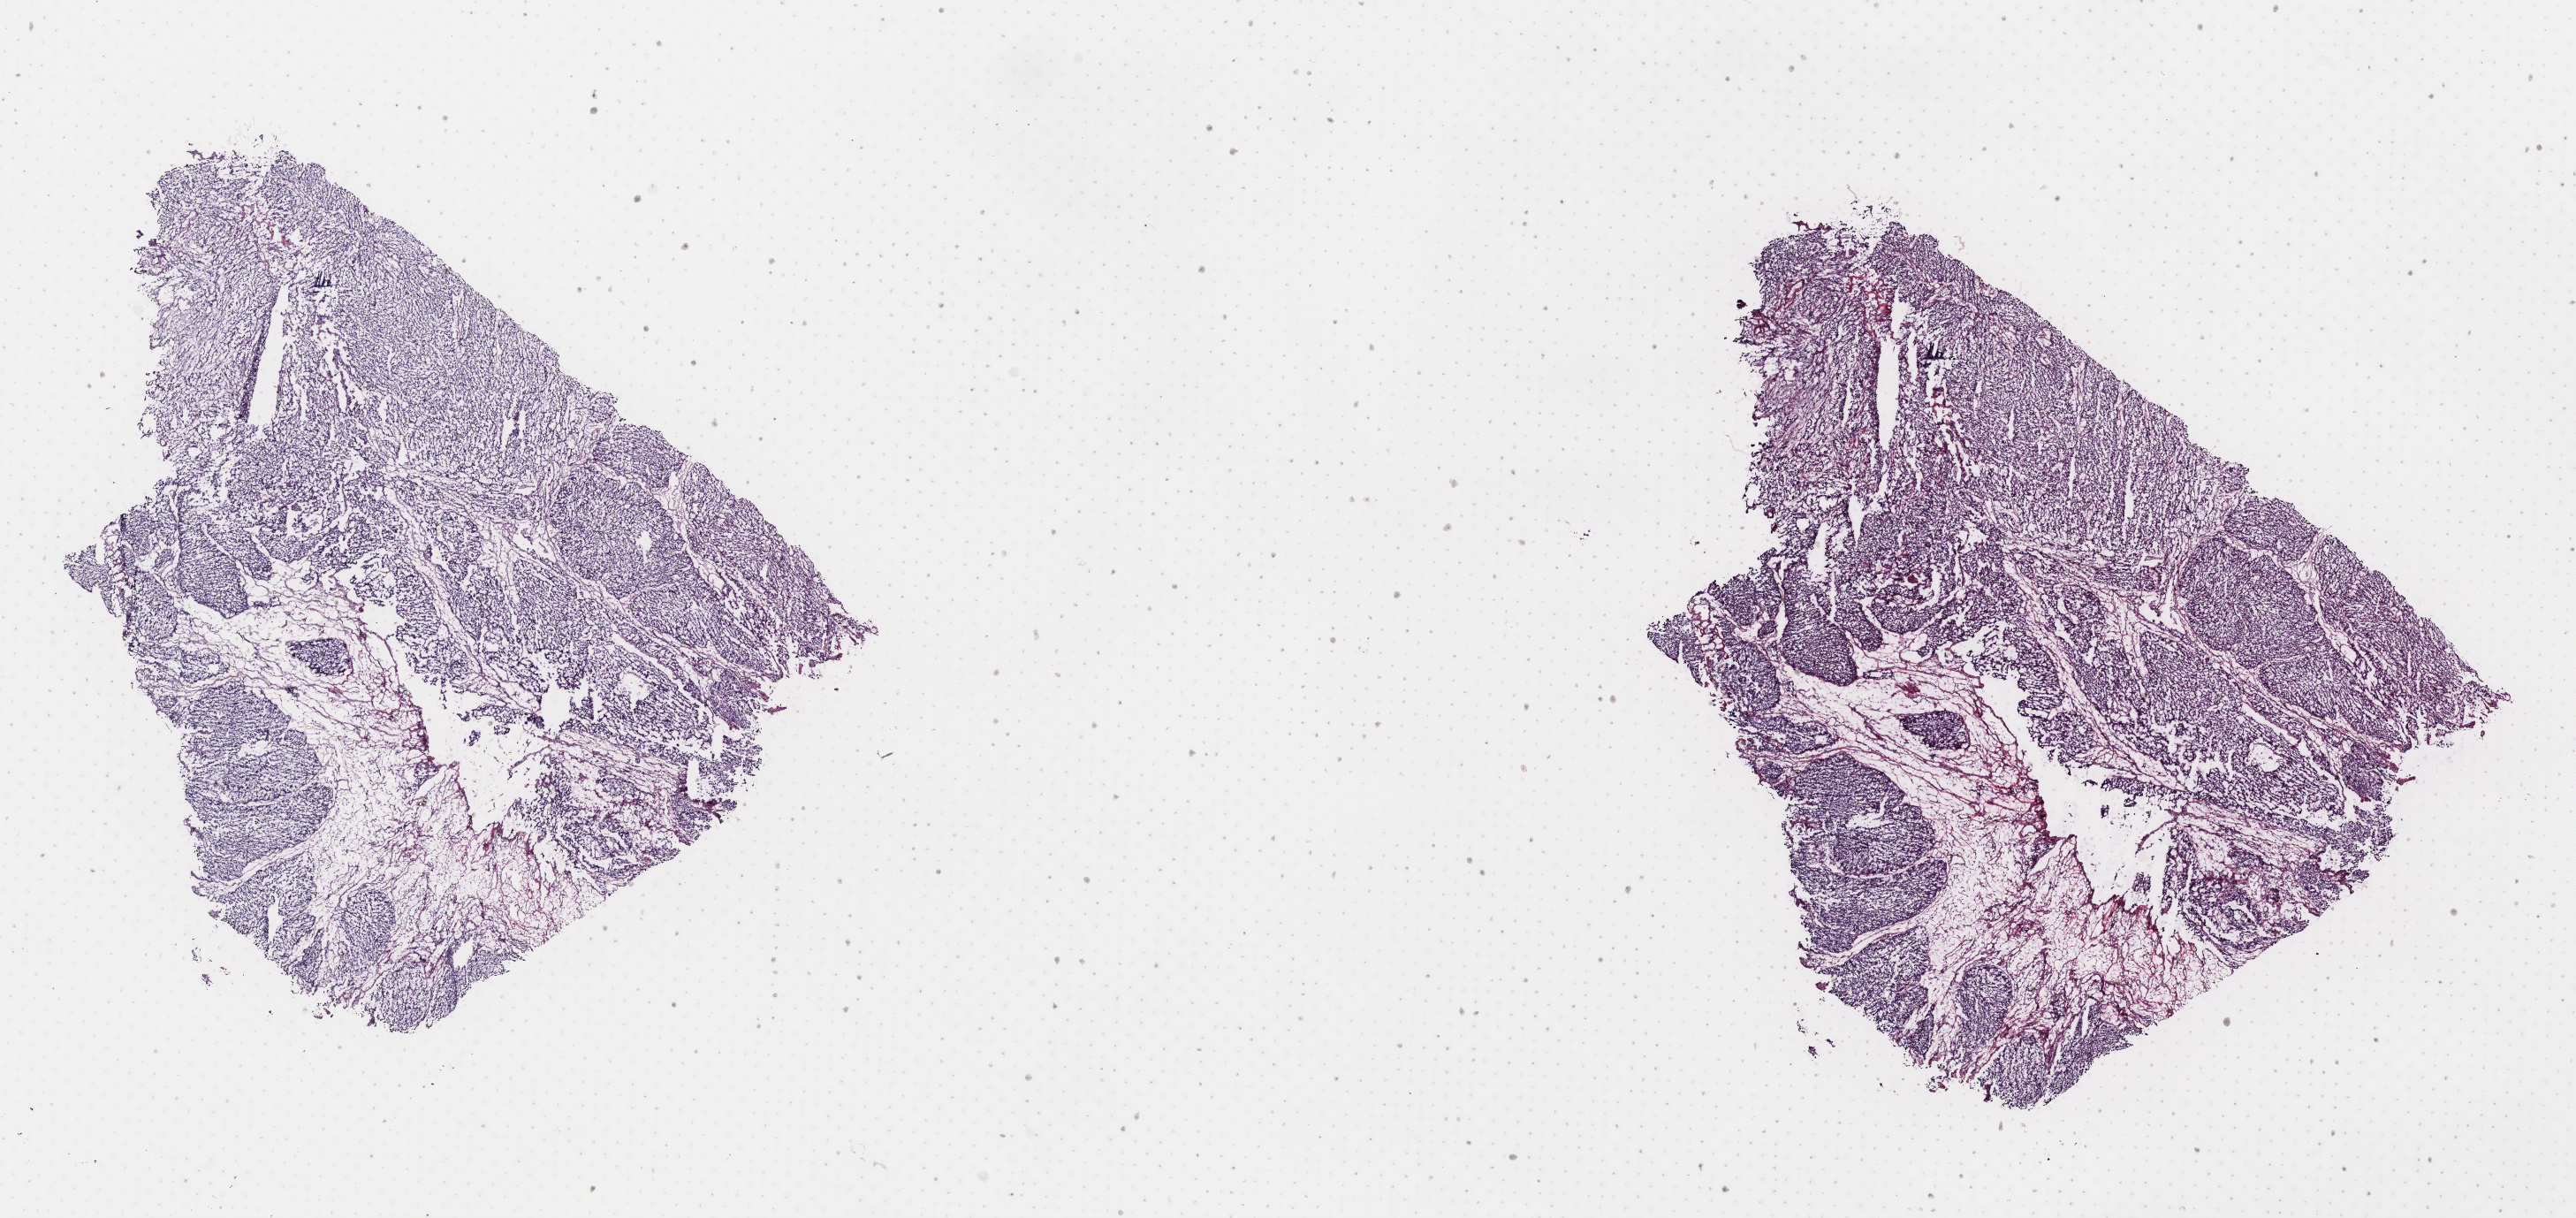
H&E whole-slide image, a low-resolution overview of the entire scanned area, about 23.0 x 10.9 mm (slide scanned at 40x); frozen section from the top of the tissue portion; sample: primary tumour, bladder. Male patient; age at initial diagnosis 64 years. Composition of this section per pathologist review: tumour cells 70%, tumour nuclei 92%.
Pathologic diagnosis: Papillary transitional cell carcinoma (lateral wall of bladder).